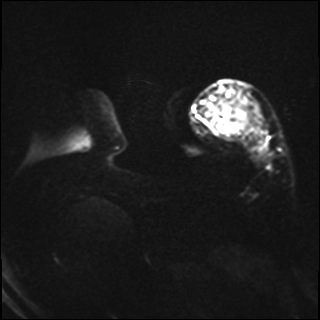
Breast MRI, one axial slice; position 6 of 37 along the scan axis; diffusion-weighted series; image 2 of 4 stored at this slice position (different b-values; order by instance number); 1.5 T; 4 mm slice thickness; 320 × 320 image matrix, field of view 320 × 320 mm. Female patient.
Structures marked on this image (outlined manually by an expert reader):
- tumour on diffusion-weighted imaging: bounding box (x1, y1, x2, y2) in pixels: (221, 102, 253, 138)